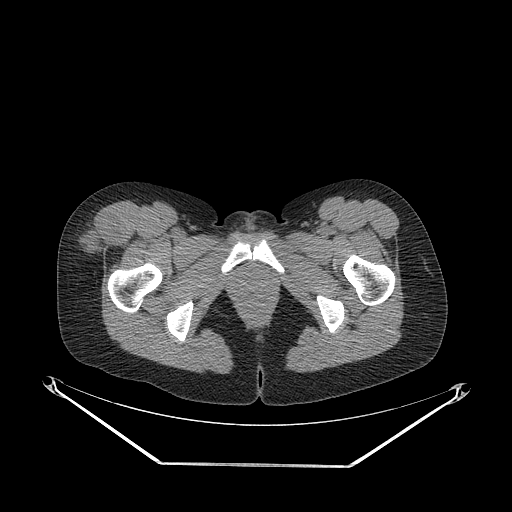
CT of an extremity soft-tissue mass (from a PET/CT study), one axial slice. Slice 56 of 267 in the series (ordered by position). Reconstruction kernel STANDARD. 140 kVp. Soft-tissue window (W 400 / L 40 HU). 3.75 mm slice thickness. 512 × 512 image matrix, field of view 500 × 500 mm. Female patient. Case-level facts recorded for this patient, not image findings: histological type: synovial sarcoma; grade: intermediate; site of the primary tumour: right thigh.
Structures marked on this image (expert contour drawn on MRI and transferred to this co-registered scan by the dataset authors):
- gross tumour volume including surrounding oedema: bounding box [x1, y1, x2, y2] px = [75, 215, 120, 254]
- gross tumour volume (mass): [75, 215, 120, 254]